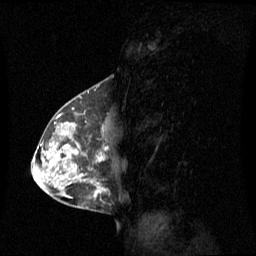
Breast MRI (dynamic contrast-enhanced), one sagittal slice; slice 34 of 60 in the series (ordered by position); dynamic contrast-enhanced series, image 2 of 3 at this slice position (ordered by acquisition); 1.5 T; TE 4.2 ms, TR 8.4 ms; 256 × 256 image matrix, field of view 270 × 270 mm. Female patient, age 42 years. From the clinical record (not read from this slice): setting: breast cancer imaged before/during neoadjuvant chemotherapy; receptor status: HR-positive, HER2-negative.
Outlined on this slice (semi-automatic segmentation, software-assisted and operator-edited):
- analysis volume of interest (the breast-tissue region the enhancement analysis was run in; not a lesion): bounding box (x1, y1, x2, y2) in pixels: (56, 113, 107, 185)
- tumour enhancement mask (voxels above the 70 % enhancement threshold inside the analysis volume of interest): (67, 147, 107, 161)